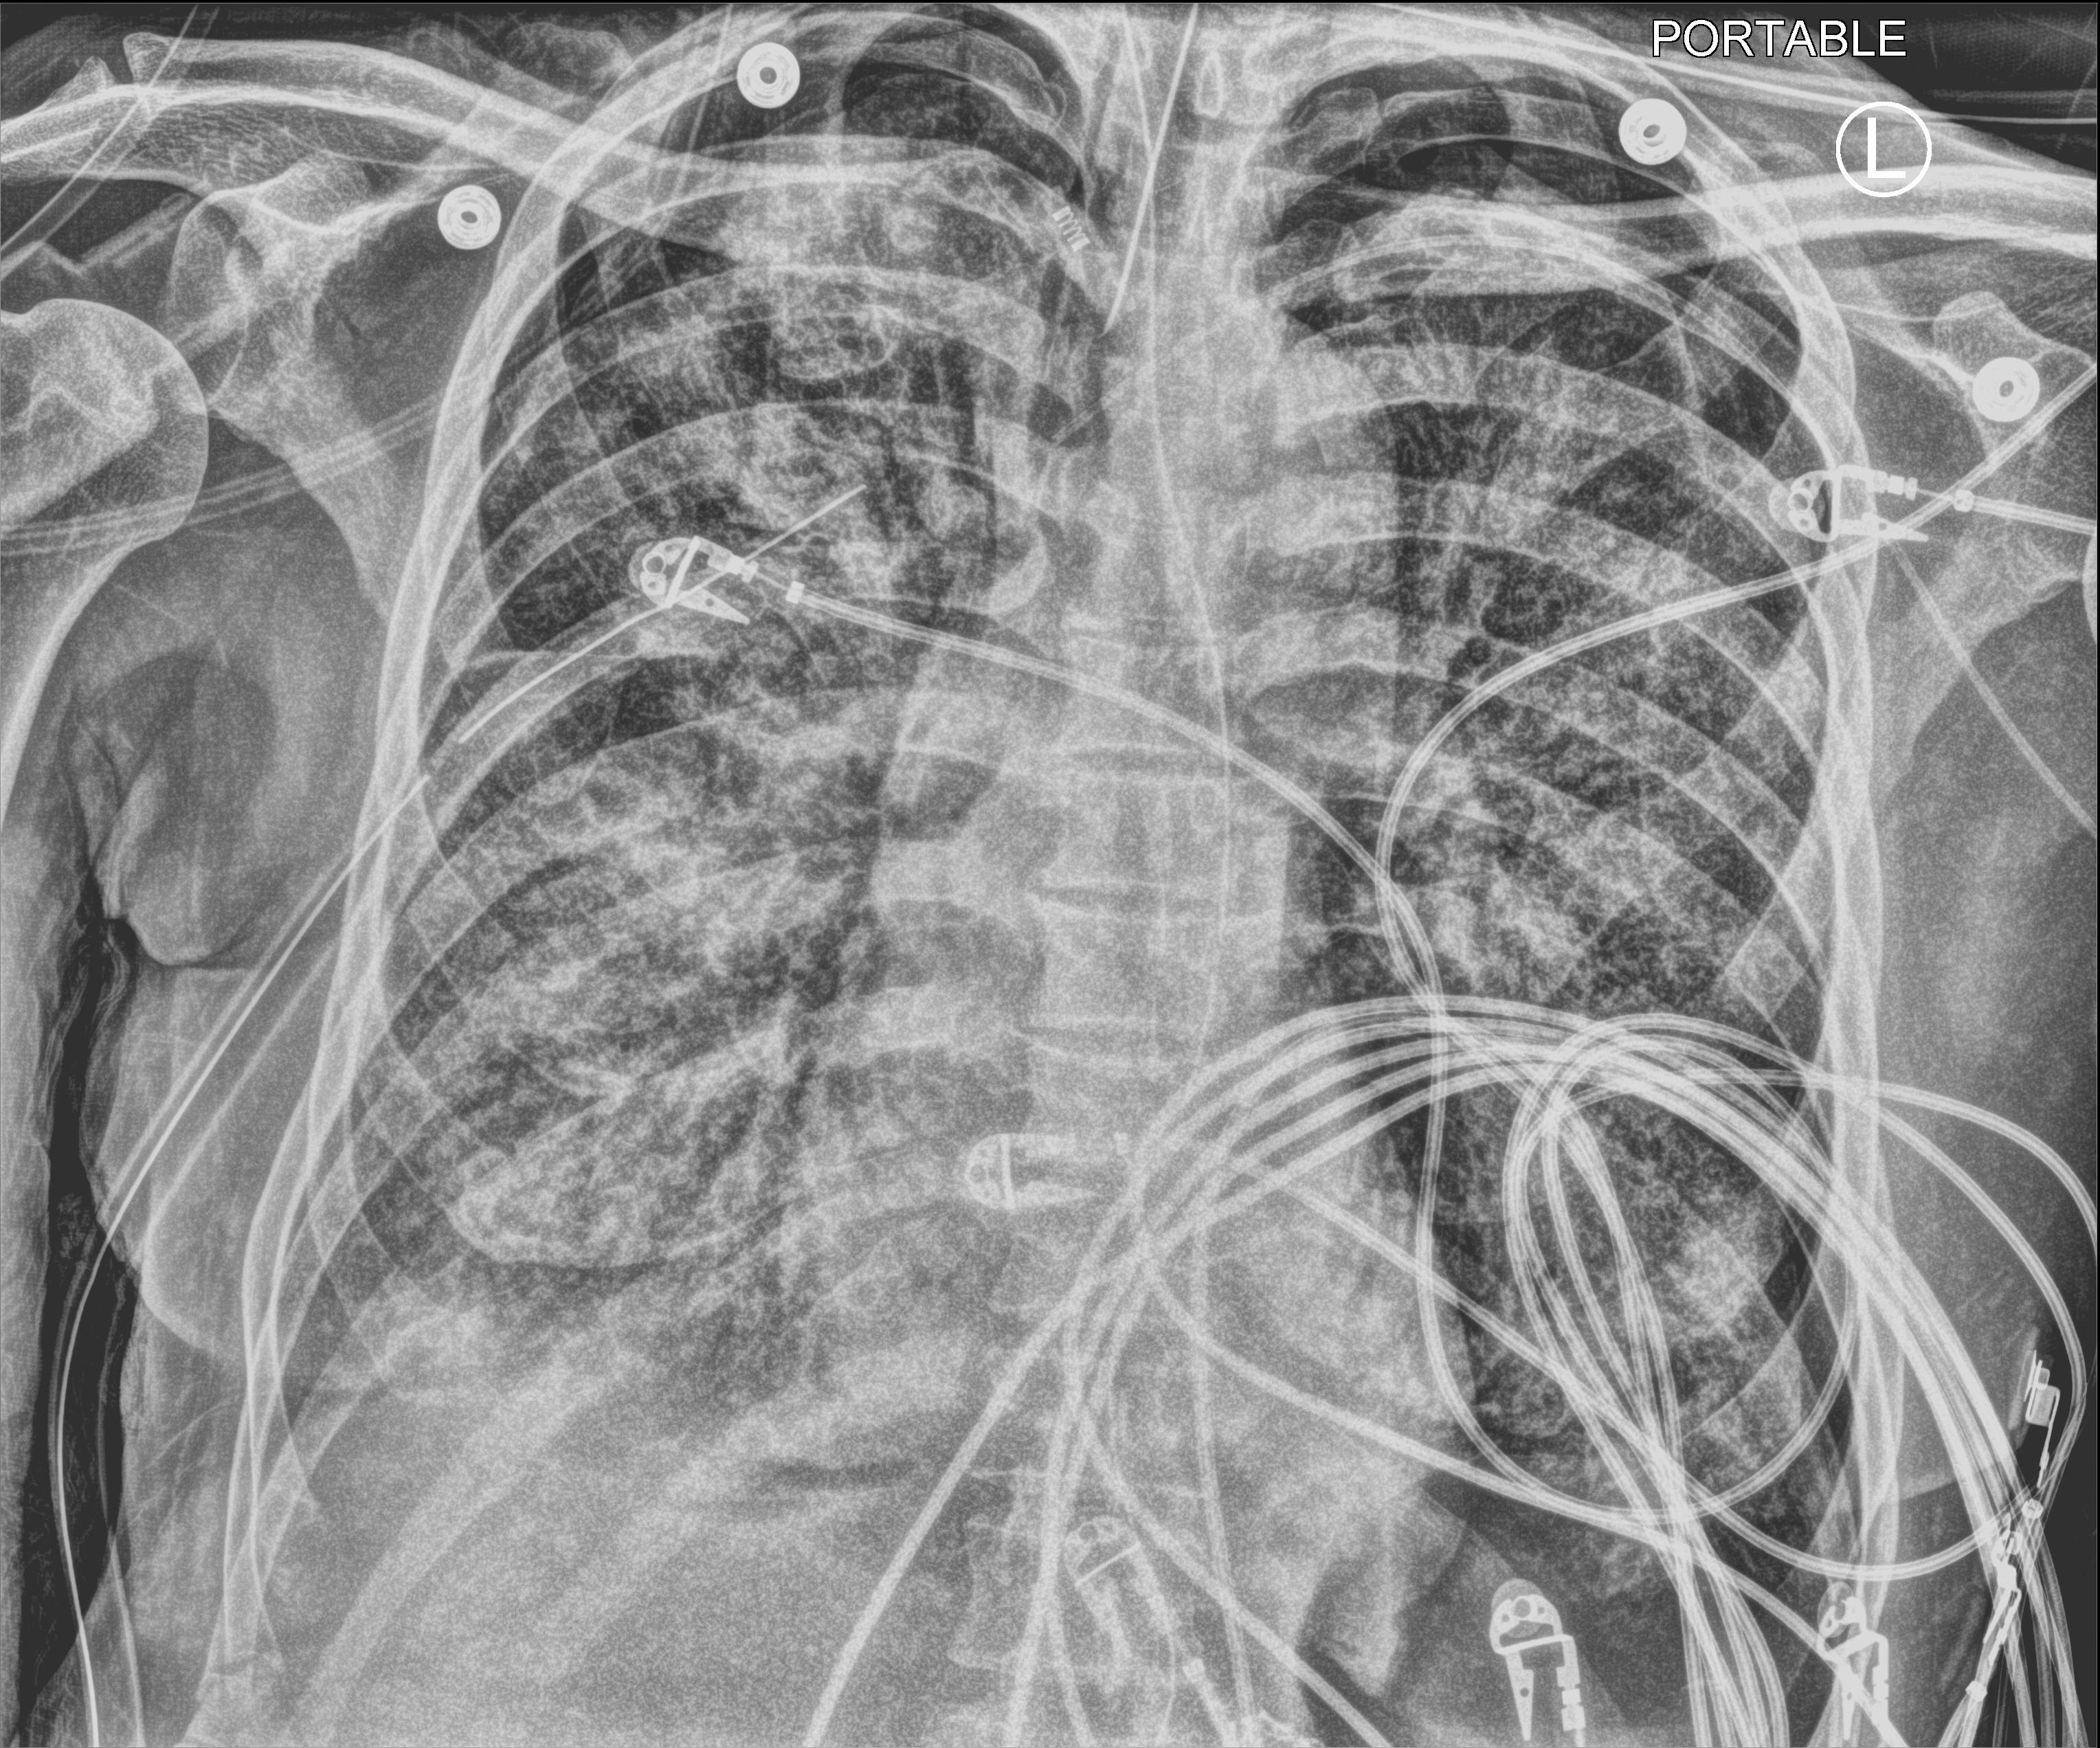
Bedside chest radiograph (computed radiography); anteroposterior (AP) projection. Male patient hospitalised with COVID-19, age 60–74 years.
Admission-level facts for this patient (not findings on this image; timing relative to this image not recorded):
- diabetes (admission record): no